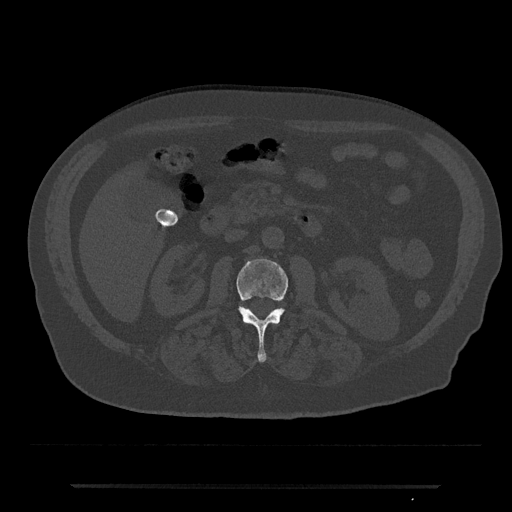
CT including the spine, one axial slice. Position 467 of 797 along the scan axis. Reconstruction kernel Br40s/3. Bone window (W 1800 / L 400 HU). 0.5 mm slice thickness. 512 × 512 image matrix. Male patient, age 80 years. Case-level facts recorded for this patient, not image findings: primary cancer: prostate; vertebrae with lytic lesions (as recorded): L1, T11.
Annotated regions visible in this slice (semi-automatically segmented with operator editing):
- L2 vertebra: bounding box <236,259,288,363> (left, top, right, bottom; pixels)